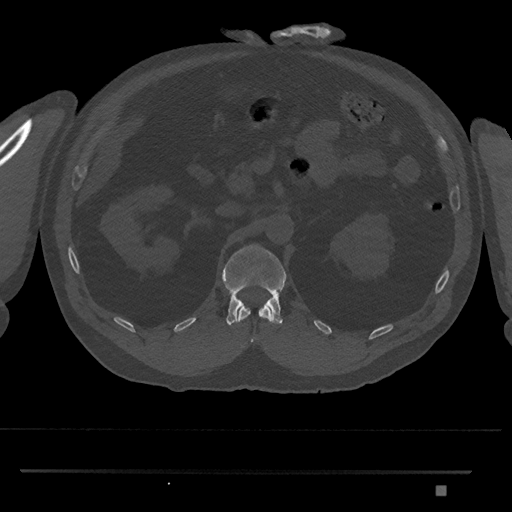
CT including the spine, one axial slice. Slice 848 of 1134 in the series (ordered by position). Reconstruction kernel Br40s/3. Bone window (W 1800 / L 400 HU). 0.5 mm slice thickness. 512 × 512 image matrix. Patient: male, 65 years. Case-level facts recorded for this patient, not image findings: primary cancer: prostate.
Annotated regions visible in this slice (semi-automatic segmentation, software-assisted and operator-edited):
- L1 vertebra: bounding box (x1, y1, x2, y2) in pixels: (222, 244, 287, 326)
- T12 vertebra: (238, 305, 272, 343)